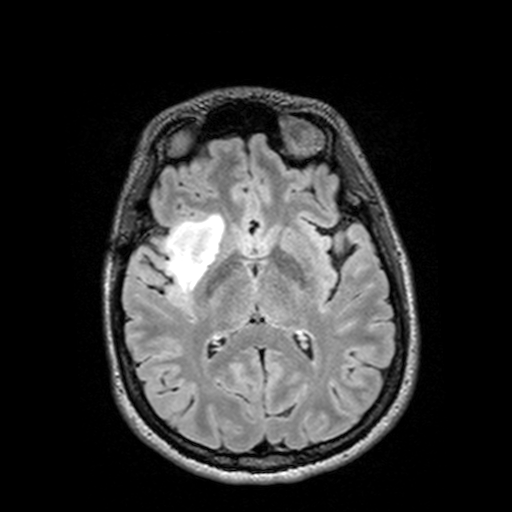
Brain MRI from a brain-tumour surgery series, one axial slice. Slice 70 of 144 in the series (ordered by position). T2 FLAIR. 1 mm slice thickness. 512 × 512 image matrix, field of view 250 × 250 mm. From the clinical record (not read from this slice): histopathology: Astrocytoma; WHO grade: 3; IDH mutation: yes; tumour location: Right Insular Temporal.
Structures marked on this image (outlined manually by an expert reader):
- tumour: bounding box (x1, y1, x2, y2) in pixels: (126, 213, 232, 294)